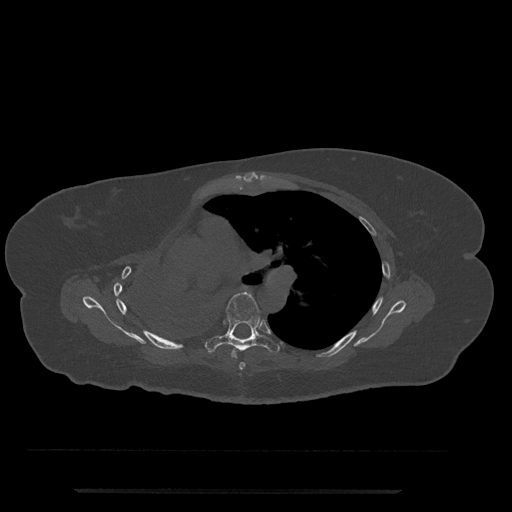
CT including the spine, one axial slice; slice 502 of 797 in the series (ordered by position); bone window (W 1800 / L 400 HU); 0.5 mm slice thickness; 512 × 512 image matrix, field of view 440 × 440 mm. Patient: female, 51 years. Case-level facts recorded for this patient, not image findings: primary cancer: neuro; vertebrae with lytic lesions (as recorded): T8.
Outlined on this slice (semi-automatic segmentation, software-assisted and operator-edited):
- T5 vertebra: bounding box (x1, y1, x2, y2) in pixels: (239, 362, 246, 370)
- T6 vertebra: (206, 292, 280, 359)